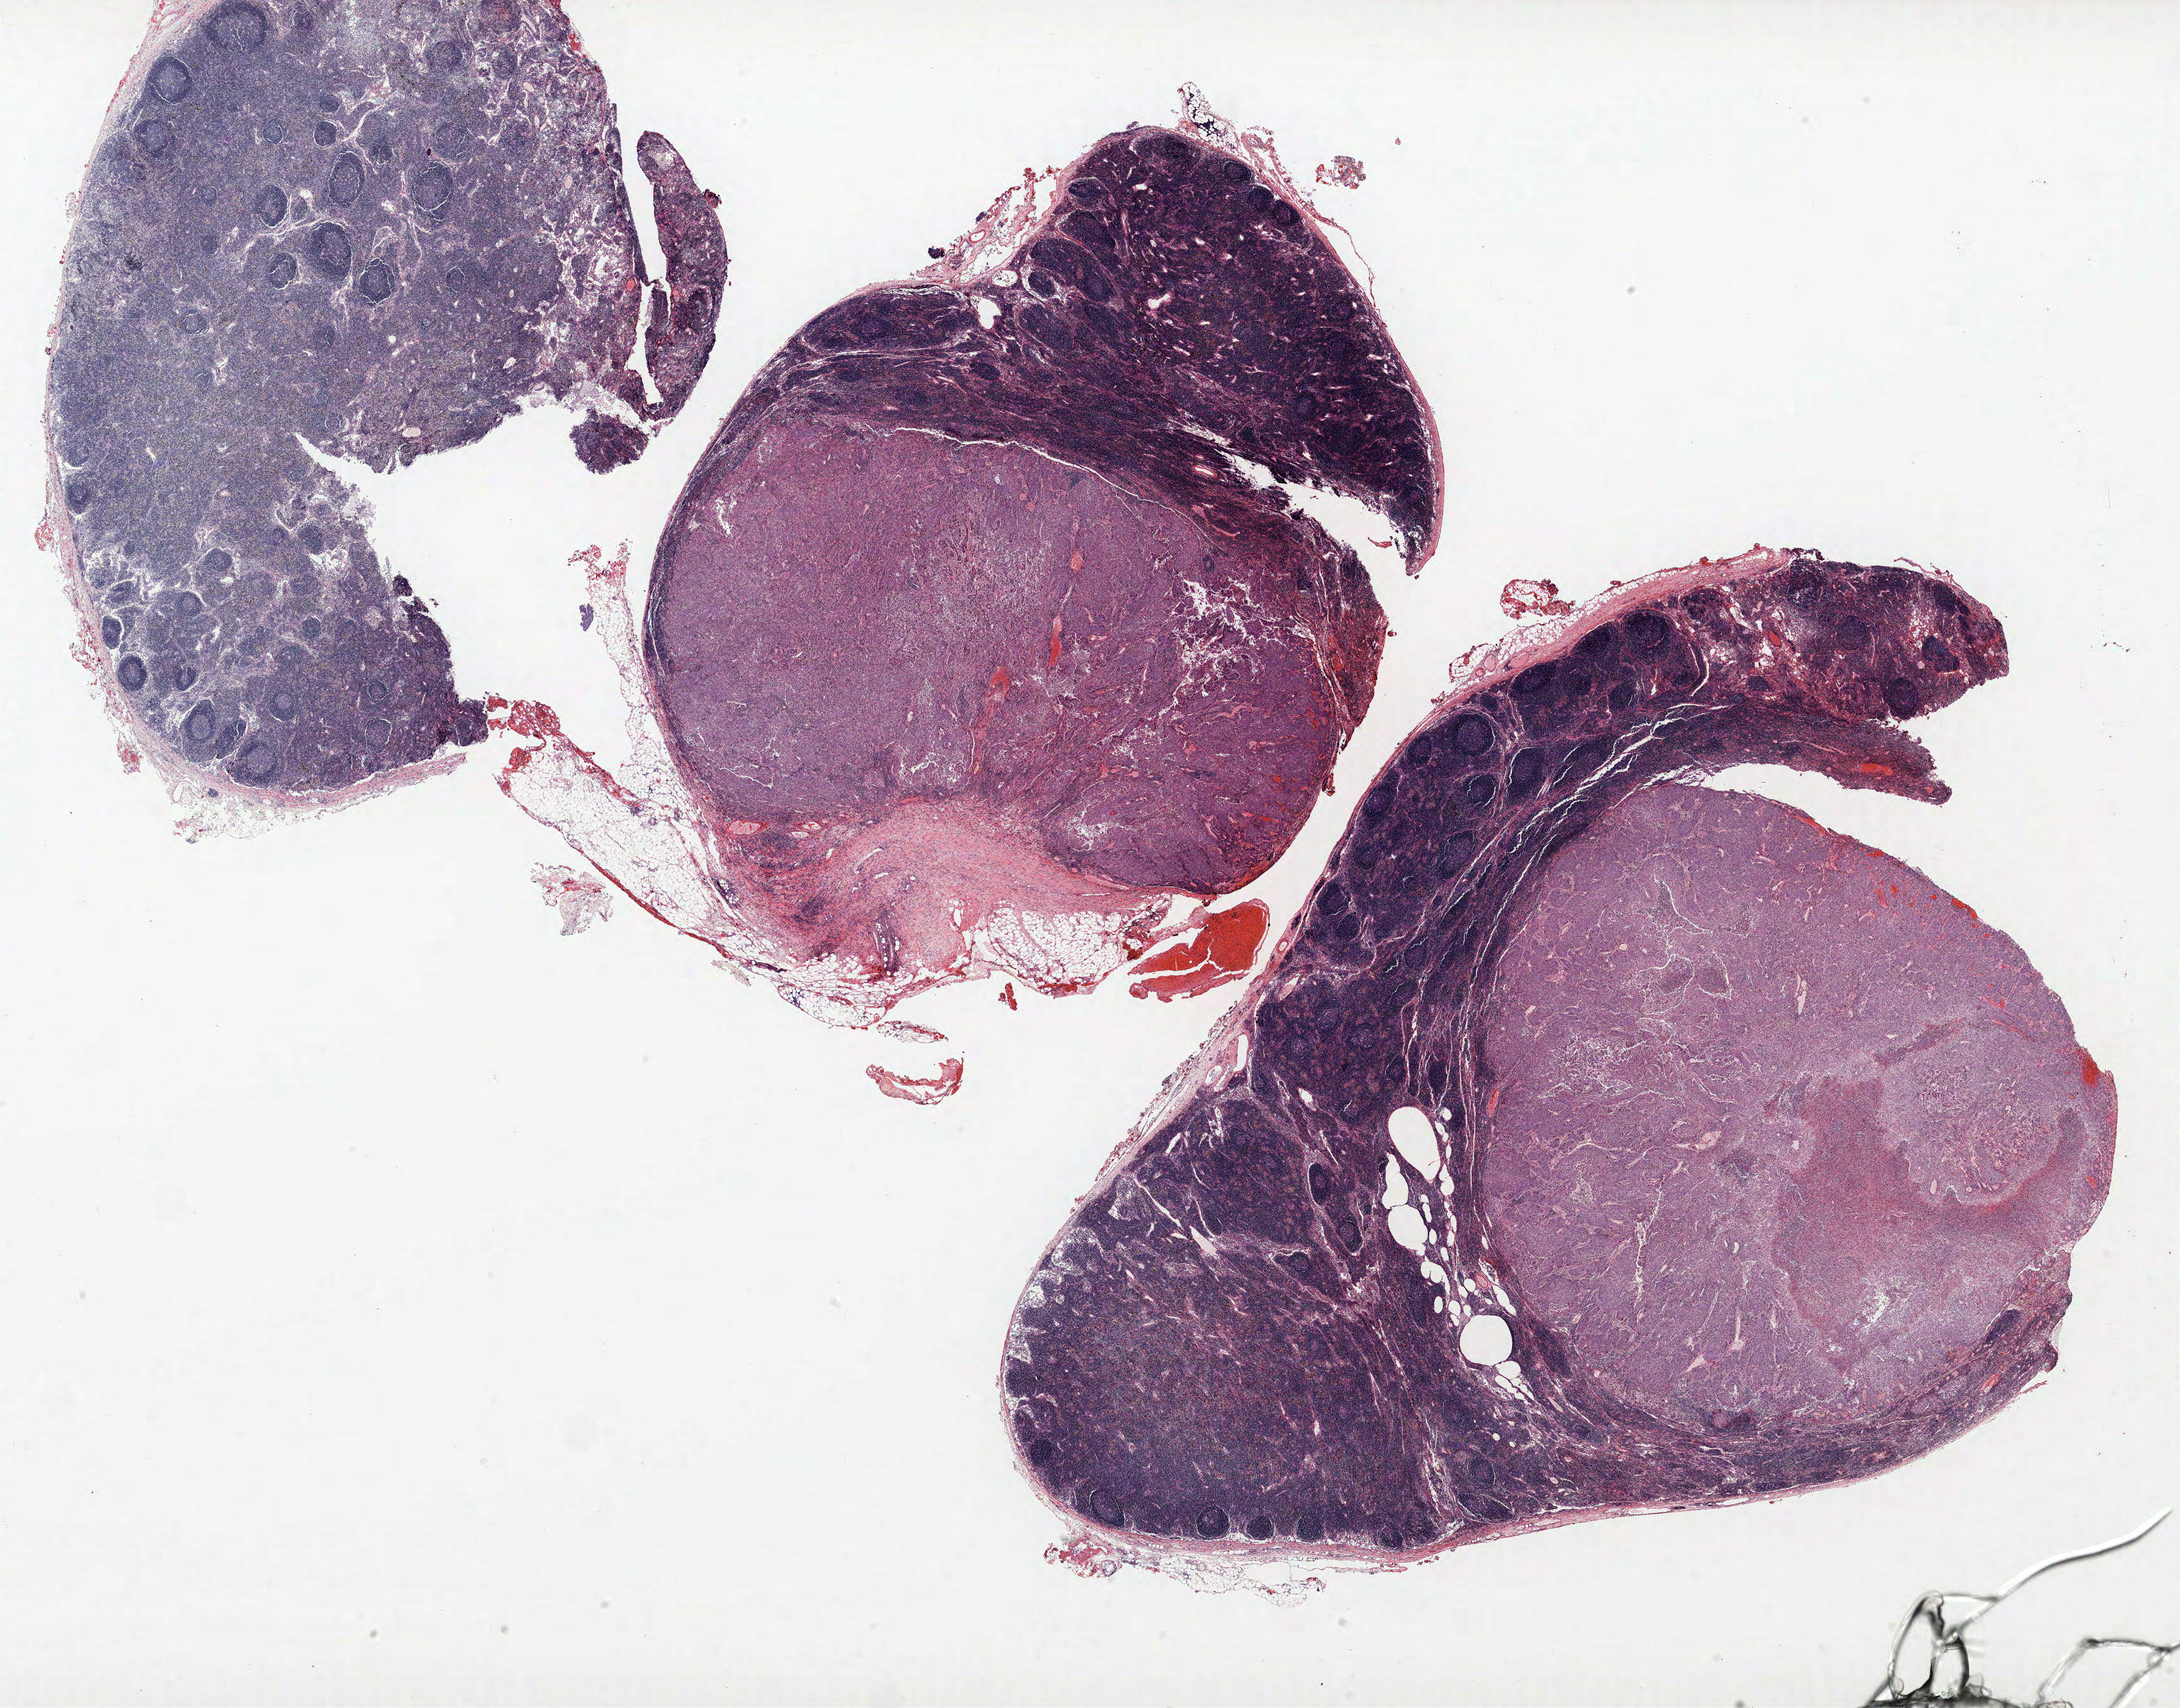
Whole-slide histology image, Hematoxylin and eosin (H&E) stained — whole scanned area (about 27.4 x 21.4 mm, acquisition: 40x scan) shown as a low-resolution overview; formalin-fixed paraffin-embedded (FFPE) section; lung tissue. Male patient, aged 62 at enrolment. Grade: moderately differentiated (G2).
• primary tumour location (clinical record): left lower lobe
• stage (AJCC 6th edition): IIIB
• participant's lung-cancer diagnosis: Bronchiolo-alveolar adenocarcinoma, NOS (ICD-O-3 8250/3)
• tumour size (pathology): 58 mm
• ICD-O-3 topography: lower lobe of lung (C34.3)